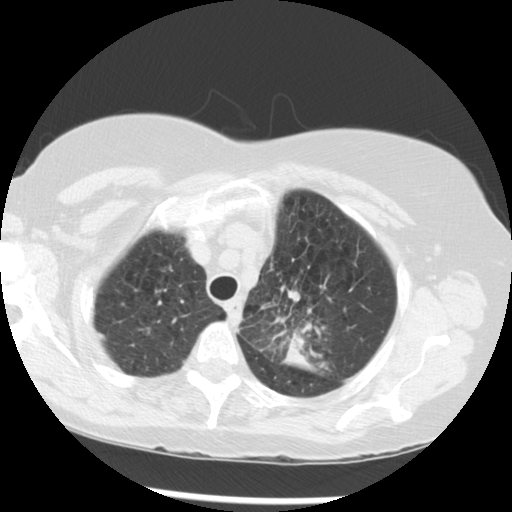
Low-dose screening chest CT, one axial slice. Slice 232 of 283 in the series (ordered by position). Reconstruction kernel STANDARD. Lung window (W 1500 / L -600 HU). 2.5 mm slice thickness. 512 × 512 image matrix, field of view 330 × 330 mm.
Annotated regions visible in this slice (manually delineated by an expert):
- lesion 1 (tumor, upper lobe of left lung): box from (x=279, y=289) to (x=320, y=373) px